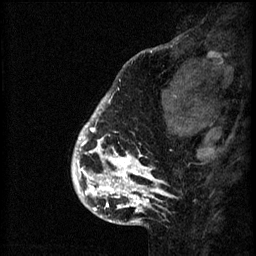
Breast MRI (dynamic contrast-enhanced), one sagittal slice; slice 14 of 60 in the series (ordered by position); 3 images stored at this slice position (order not interpretable as contrast timing); 1.5 T; TE 4.2 ms, TR 8.2 ms; 2 mm slice thickness; 256 × 256 image matrix, field of view 180 × 180 mm. Patient: female, 41 years.
Outlined on this slice (semi-automatic segmentation, software-assisted and operator-edited):
- analysis volume of interest (the breast-tissue region the enhancement analysis was run in; not a lesion): bounding box (x1, y1, x2, y2) in pixels: (73, 108, 176, 205)
- tumour enhancement mask (voxels above the 70 % enhancement threshold inside the analysis volume of interest): (73, 108, 168, 205)